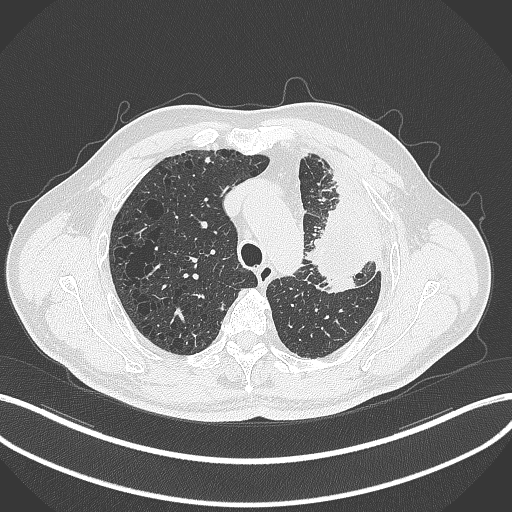
Chest CT, one axial slice. Position 240 of 297 along the scan axis. Reconstruction kernel B70f. 120 kVp. Lung window (W 1500 / L -600 HU). 512 × 512 image matrix. Patient: male, 68 years. From the clinical record (not read from this slice): clinical TNM (as recorded): T3 N3 M1.
Outlined on this slice (rectangle marked by the reading radiologist):
- lung tumour (recorded histology: adenocarcinoma): bounding box <306,194,373,293> (left, top, right, bottom; pixels)